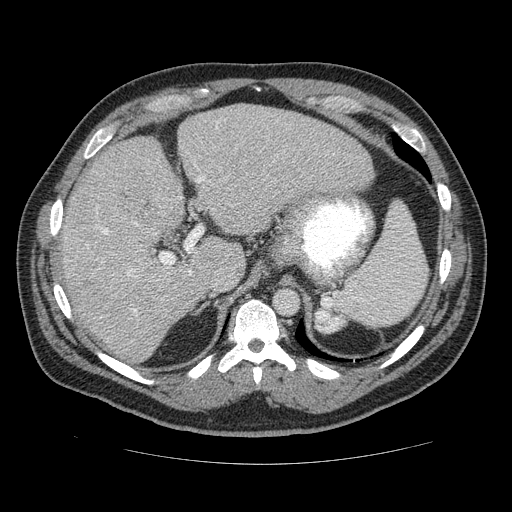
Contrast-enhanced abdominal CT (liver protocol), one axial slice. Position 90 of 113 along the scan axis. Reconstruction kernel STANDARD. Soft-tissue window (W 400 / L 40 HU). 2.5 mm slice thickness. 512 × 512 image matrix, field of view 400 × 400 mm. Case-level facts recorded for this patient, not image findings: diagnosis: hepatocellular carcinoma (patient treated with transarterial chemoembolisation; whether this scan precedes or follows treatment is not stated here); TNM stage (as recorded): Stage-II; Child-Pugh class: B; tumour nodularity: multinodular; tumour size: 4.8 cm.
Structures marked on this image (semi-automatically segmented with operator editing):
- liver parenchyma outside the tumour (the mass and vessels are separate outlines, so this box may not span the whole liver): bounding box <52,106,376,362> (left, top, right, bottom; pixels)
- mass: <90,261,173,295>
- liver vessels: <84,126,294,329>